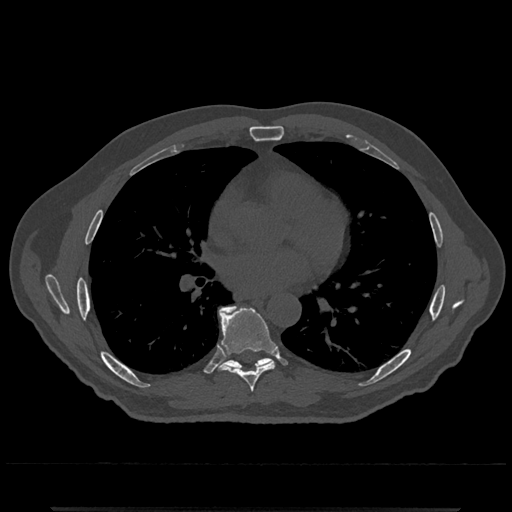
CT including the spine, one axial slice. Slice 705 of 797 in the series (ordered by position). Reconstruction kernel Br40s/3. 120 kVp. Bone window (W 1800 / L 400 HU). 0.5 mm slice thickness. 512 × 512 image matrix. Male patient, age 67 years. From the clinical record (not read from this slice): primary cancer: prostate.
Outlined on this slice (semi-automatic segmentation, software-assisted and operator-edited):
- T7 vertebra: bounding box [x1, y1, x2, y2] px = [219, 307, 276, 392]
- T8 vertebra: [218, 306, 271, 370]